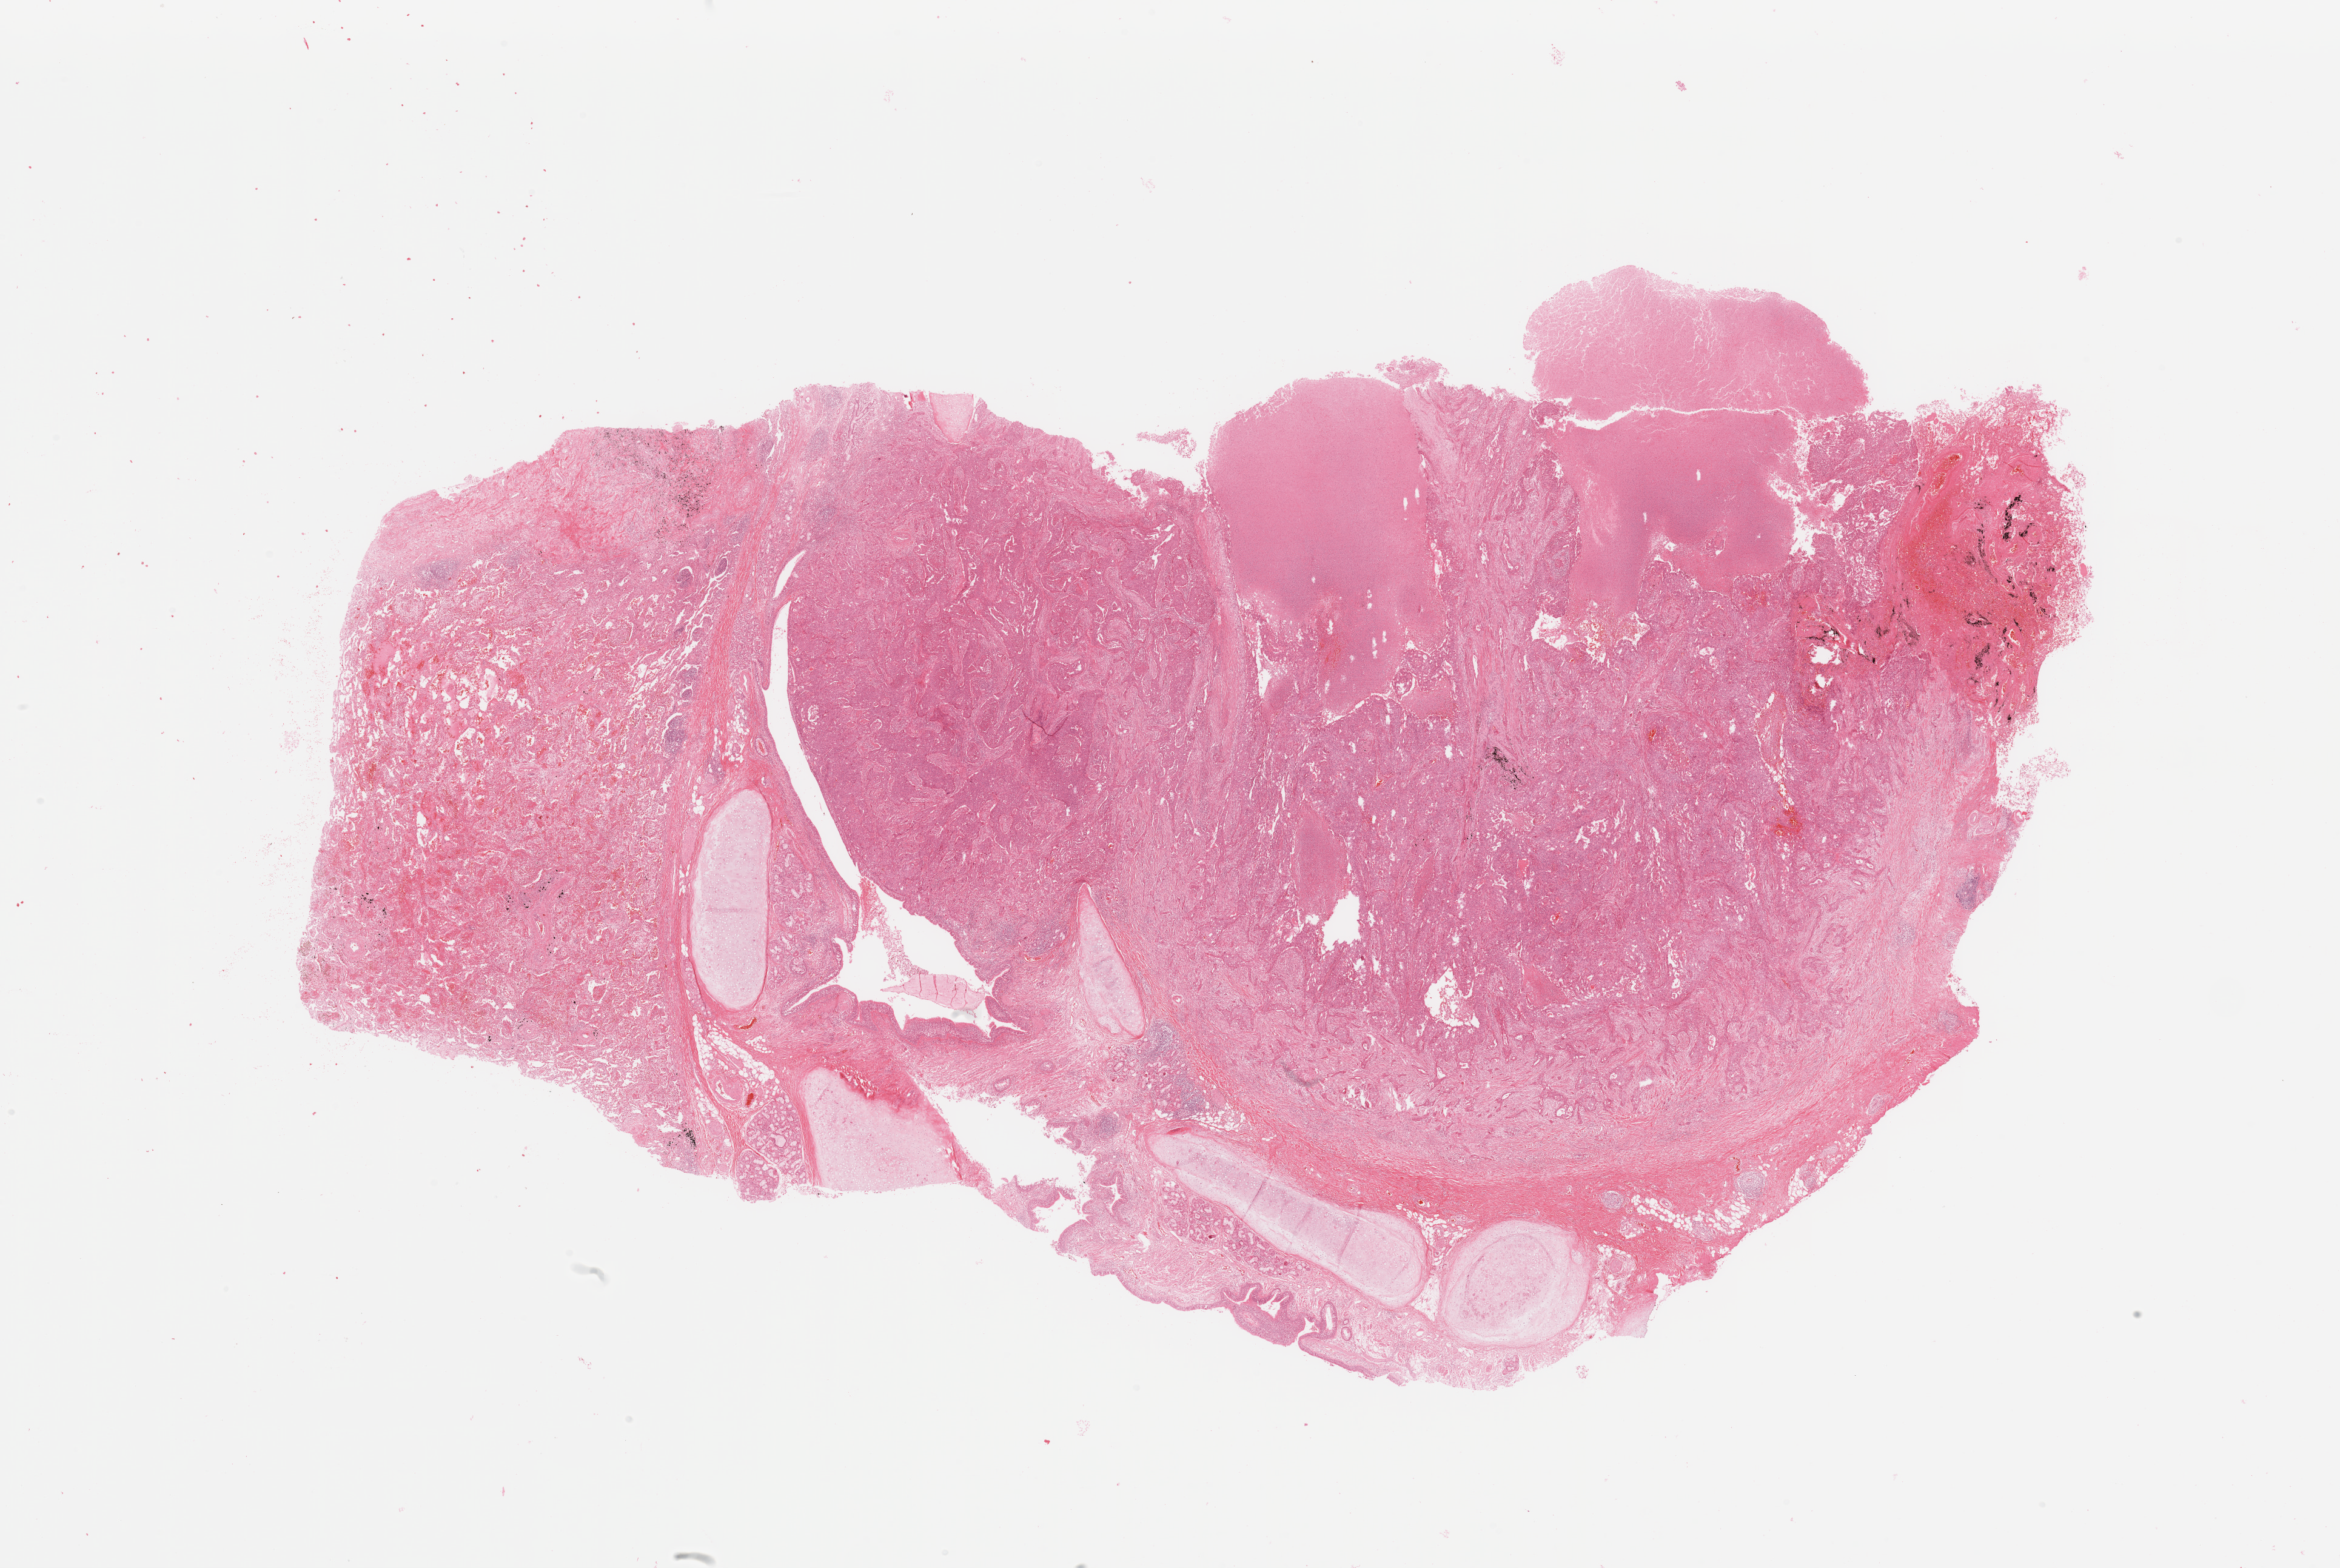
Whole-slide histology image, H&E, low-resolution overview of the scanned area, about 30.5 x 20.5 mm, lung, tumour tissue. Patient: male, age 59 years. Histologic grade: G3 (poorly differentiated).
• AJCC pathologic stage: IIA
• histologic diagnosis: Adenocarcinoma, NOS